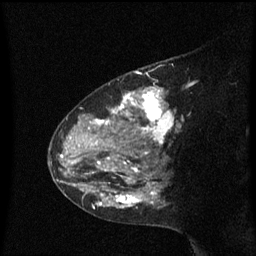
Breast MRI (dynamic contrast-enhanced), one sagittal slice; position 41 of 60 along the scan axis; dynamic contrast-enhanced series, image 2 of 3 at this slice position (ordered by acquisition); 1.5 T; TE 4.2 ms, TR 8.4 ms; 2 mm slice thickness; 256 × 256 image matrix, field of view 200 × 200 mm. Patient: female, 48 years. From the clinical record (not read from this slice): setting: breast cancer imaged before/during neoadjuvant chemotherapy; receptor status: HR-positive, HER2-negative.
Annotated regions visible in this slice (semi-automatically segmented with operator editing):
- analysis volume of interest (the breast-tissue region the enhancement analysis was run in; not a lesion): bounding box [x1, y1, x2, y2] px = [80, 80, 183, 217]
- tumour enhancement mask (voxels above the 70 % enhancement threshold inside the analysis volume of interest): [88, 88, 179, 209]